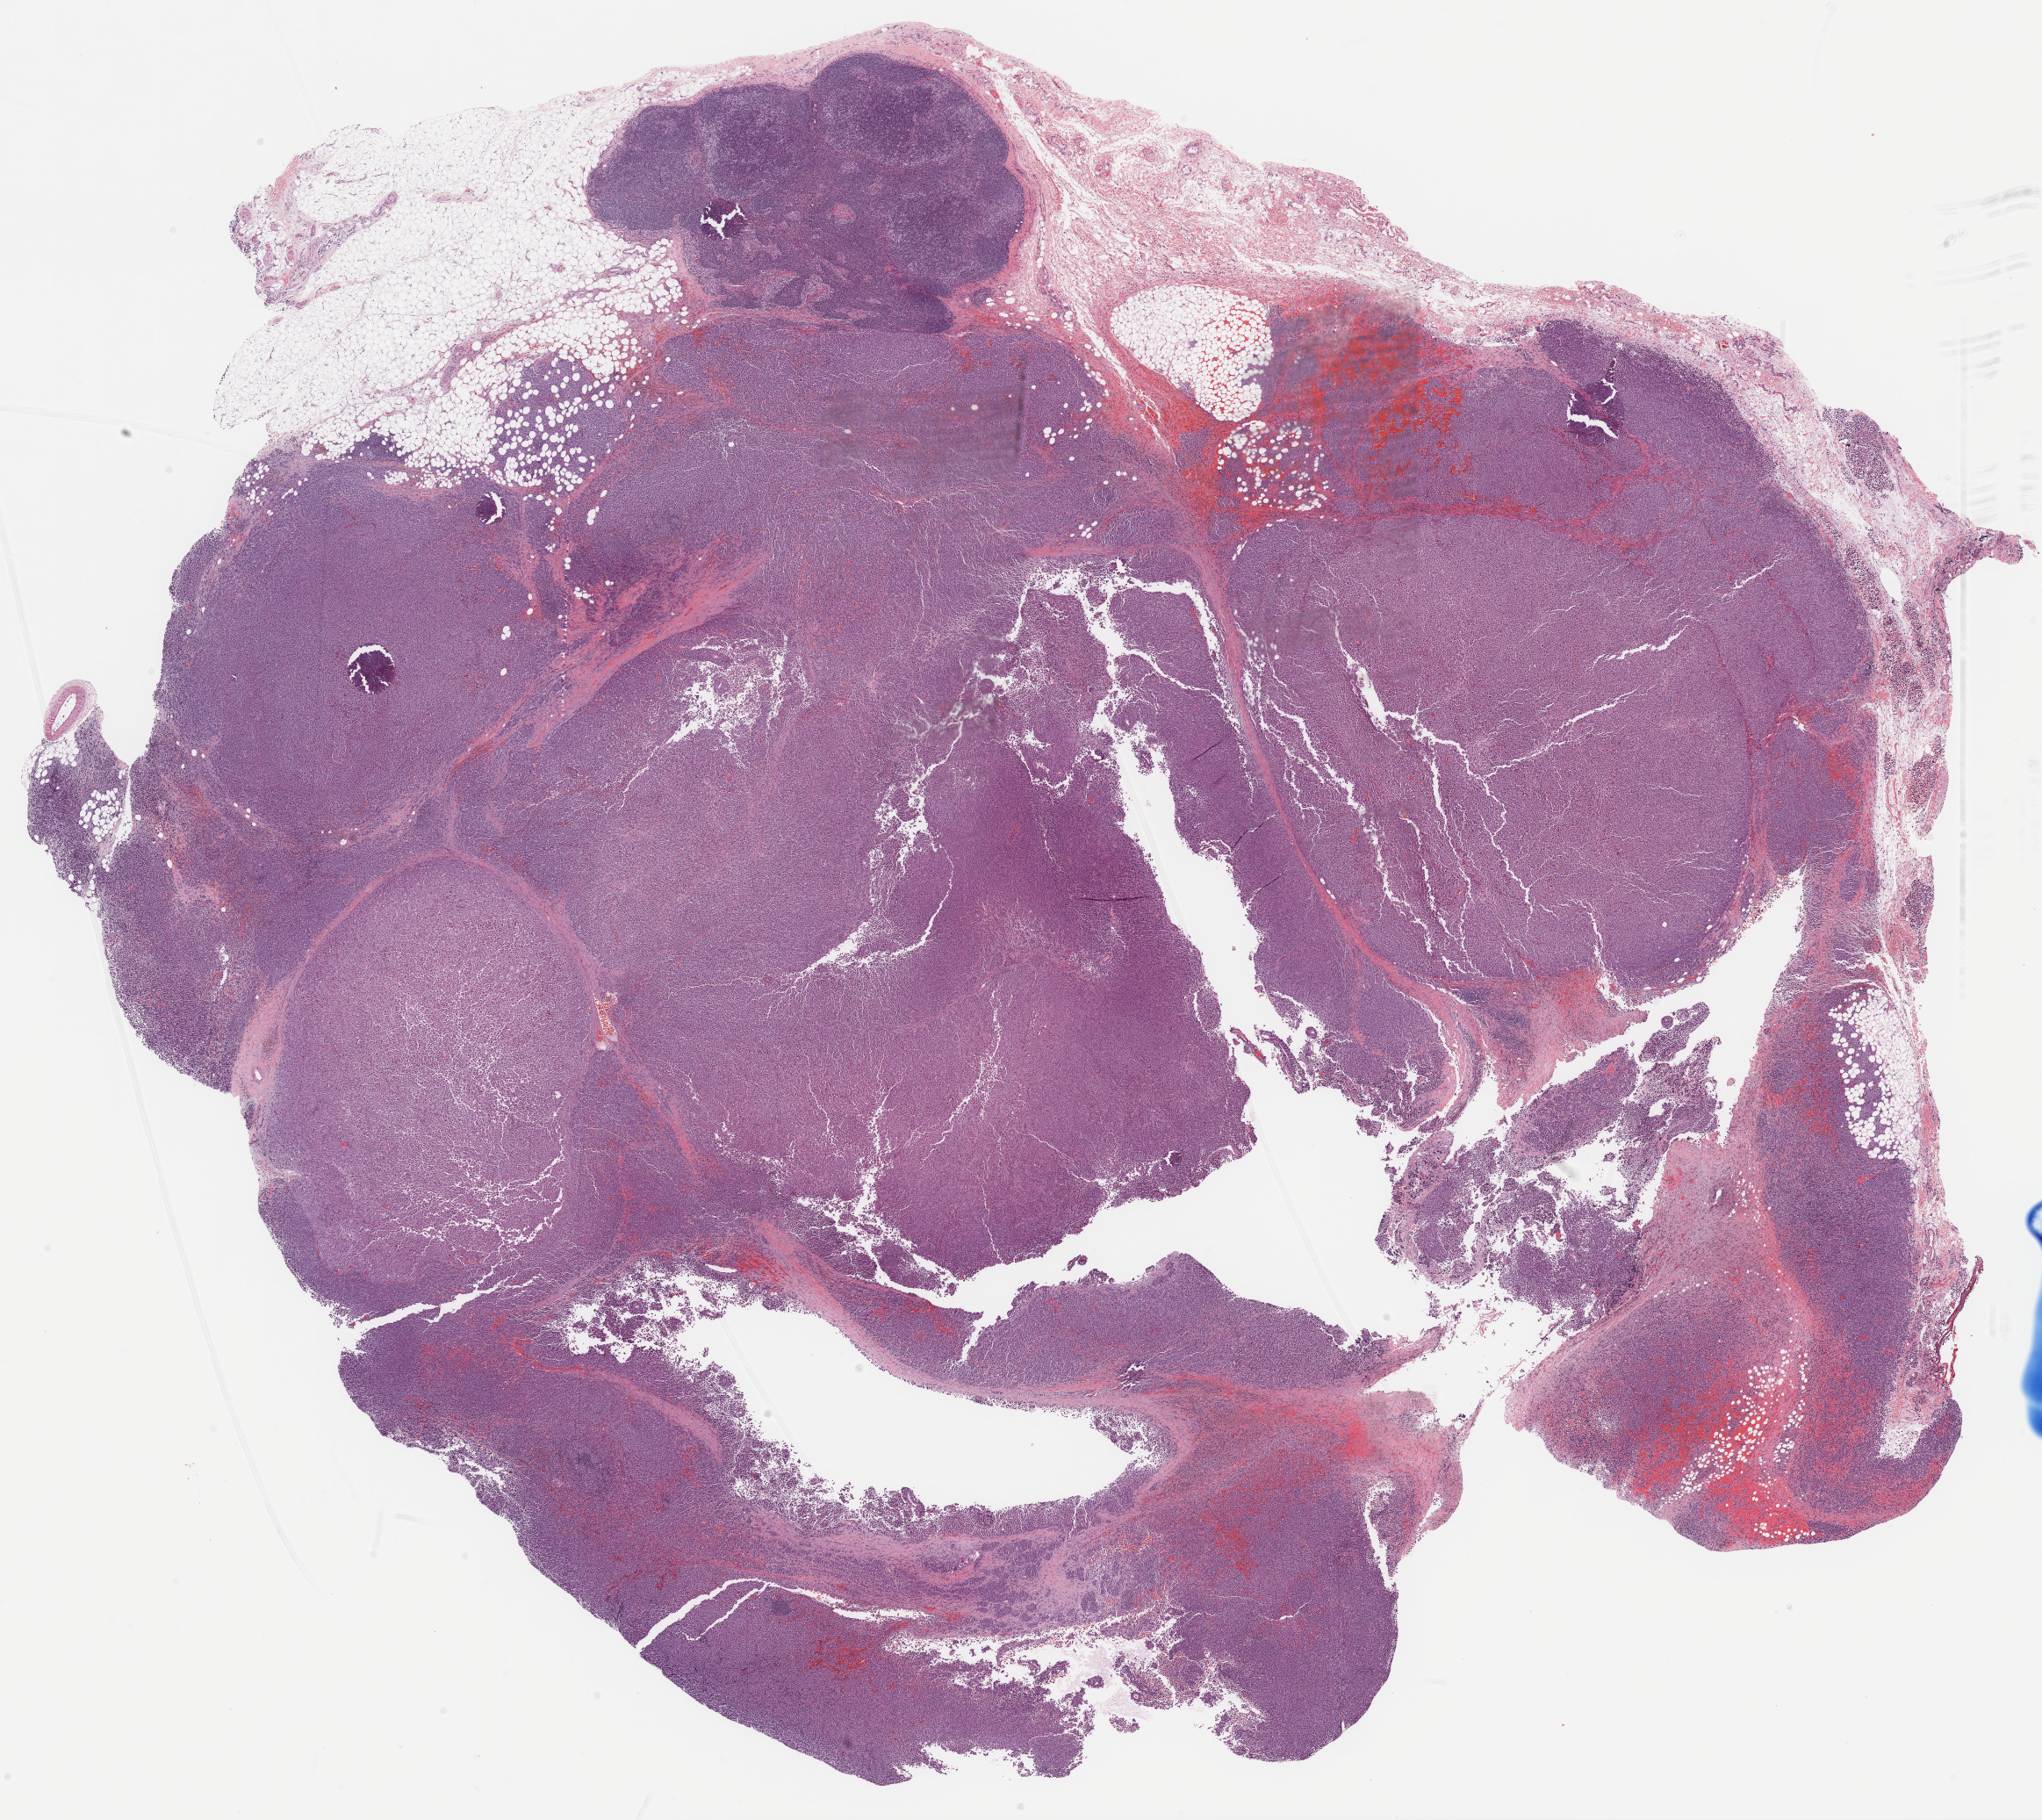
Whole-slide histology image, Hematoxylin and eosin (H&E) stained, shown as a low-resolution overview of the whole scanned area (about 18.8 x 16.7 mm, from a 20x scan). Formalin-fixed paraffin-embedded (FFPE) diagnostic section. Metastatic tumour sample. Male, age 36 years at initial diagnosis.
This section: metastatic tumour tissue. Patient diagnosis: Malignant melanoma, NOS.